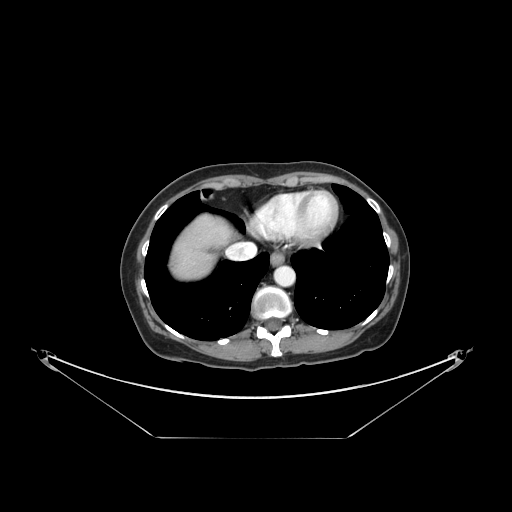
Contrast-enhanced abdominal CT, one axial slice; position 135 of 148 along the scan axis; reconstruction kernel STANDARD; 120 kVp; intravenous contrast given; soft-tissue window (W 400 / L 40 HU); 2.5 mm slice thickness; 512 × 512 image matrix, field of view 500 × 500 mm. Female patient, age 73 years. From the clinical record (not read from this slice): diagnosis: colorectal cancer liver metastases, imaged before liver resection; multiple liver metastases: no; largest metastasis: 1 cm; chemotherapy before resection: yes.
Structures marked on this image (manually delineated by an expert):
- liver: bounding box (x1, y1, x2, y2) in pixels: (172, 217, 230, 281)
- planned liver remnant (the part of the liver to remain after resection): (204, 217, 229, 237)